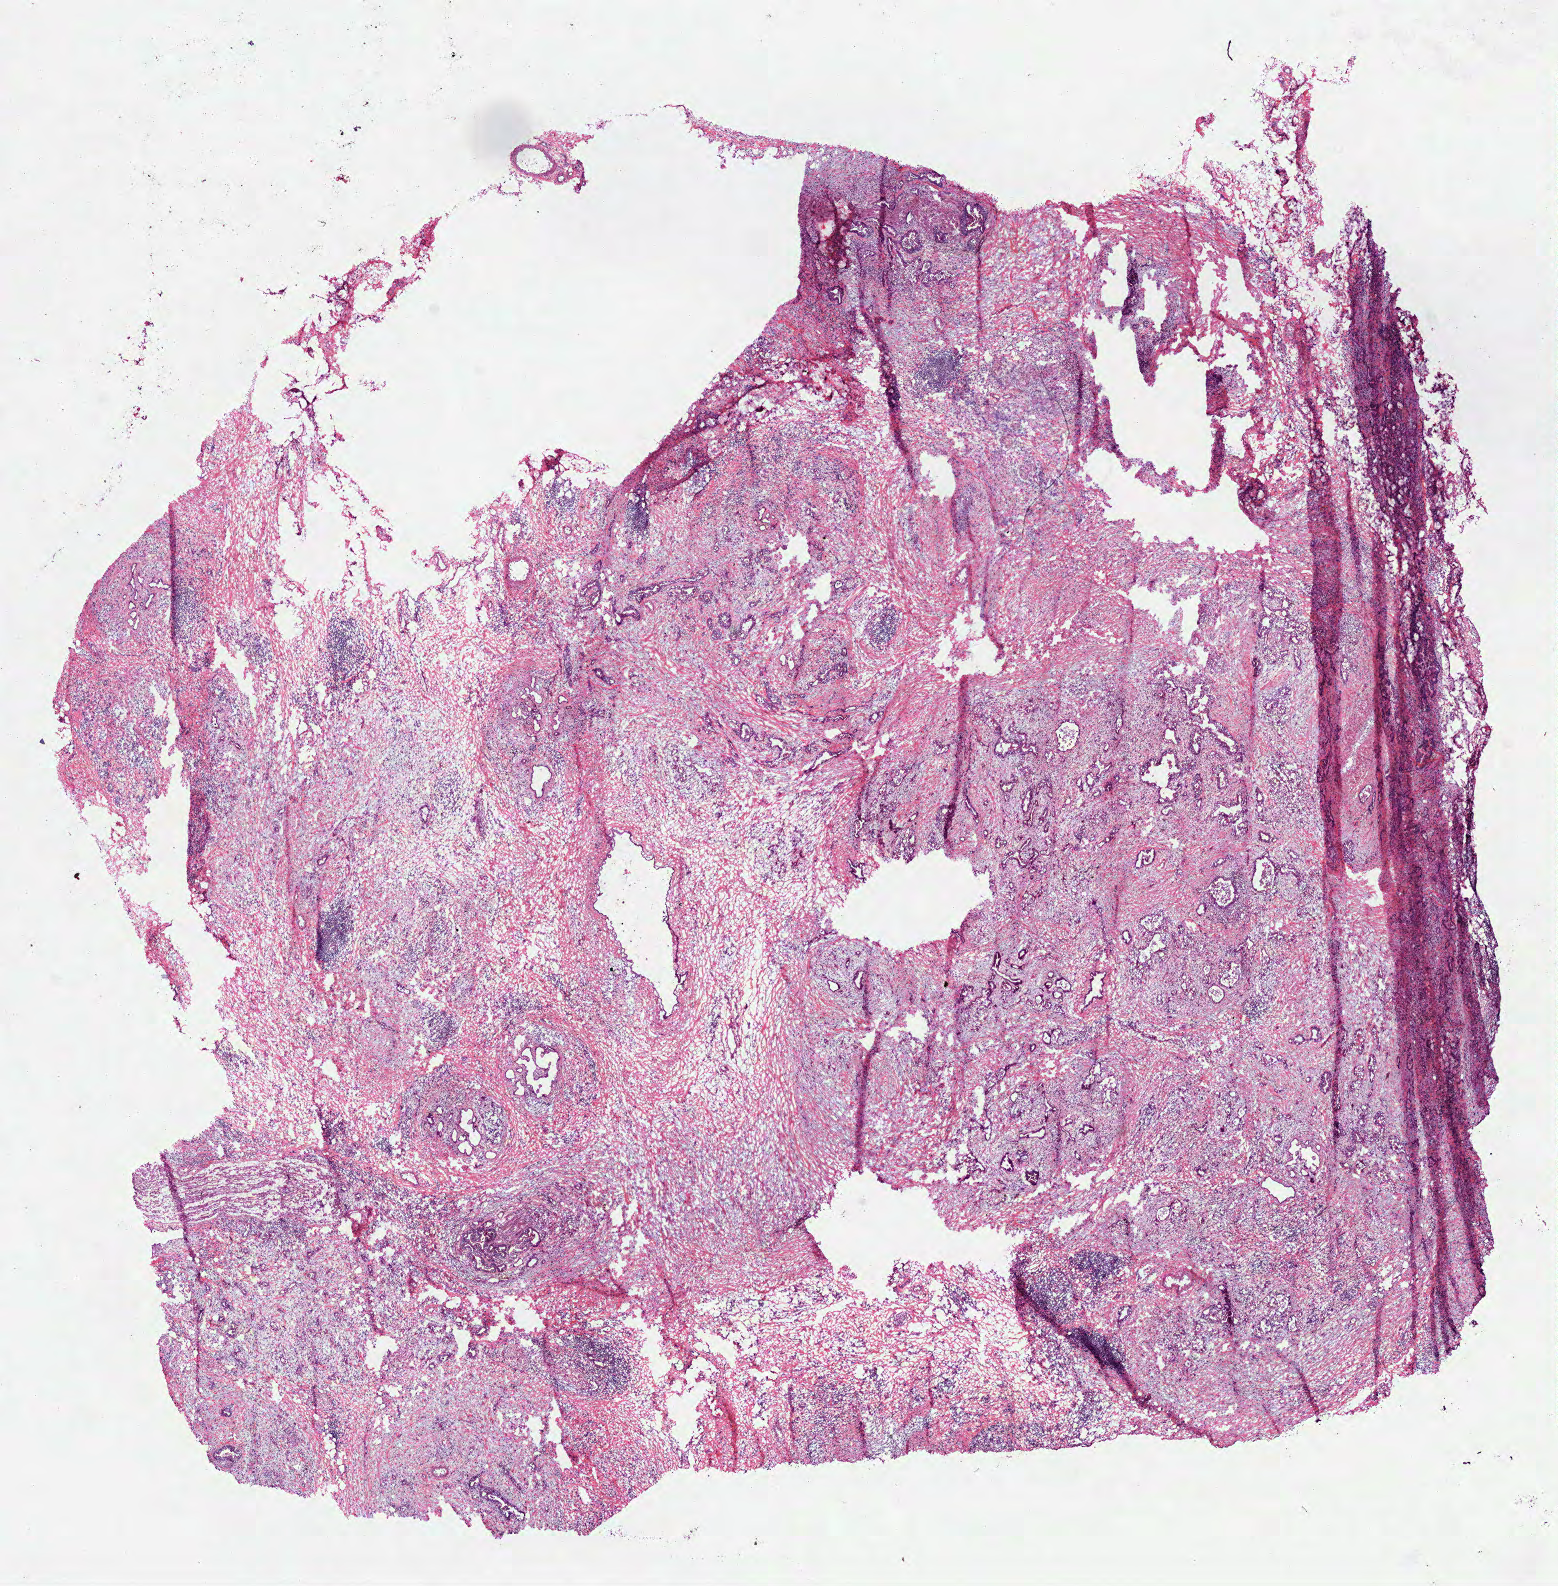
Whole-slide histology image, H&E-stained, shown as a low-resolution overview of the whole scanned area (about 12.6 x 12.8 mm, from a 40x scan), frozen section, pancreas, primary tumour sample. Patient: female, age at initial diagnosis 44 years. Histologic grade: G1 (well differentiated). Composition of this section per pathologist review: tumour cells 80%, tumour nuclei 40%, normal cells 0%, stromal cells 20%, necrosis 0%. Infiltration values recorded for this section: lymphocyte infiltration 15%, monocyte infiltration 0%, neutrophil infiltration 10%.
Pathologic diagnosis: Infiltrating duct carcinoma, NOS (head of pancreas). AJCC pathologic stage: IIB (6th edition). Lymph nodes positive (case pathology): 5 of 17 examined.